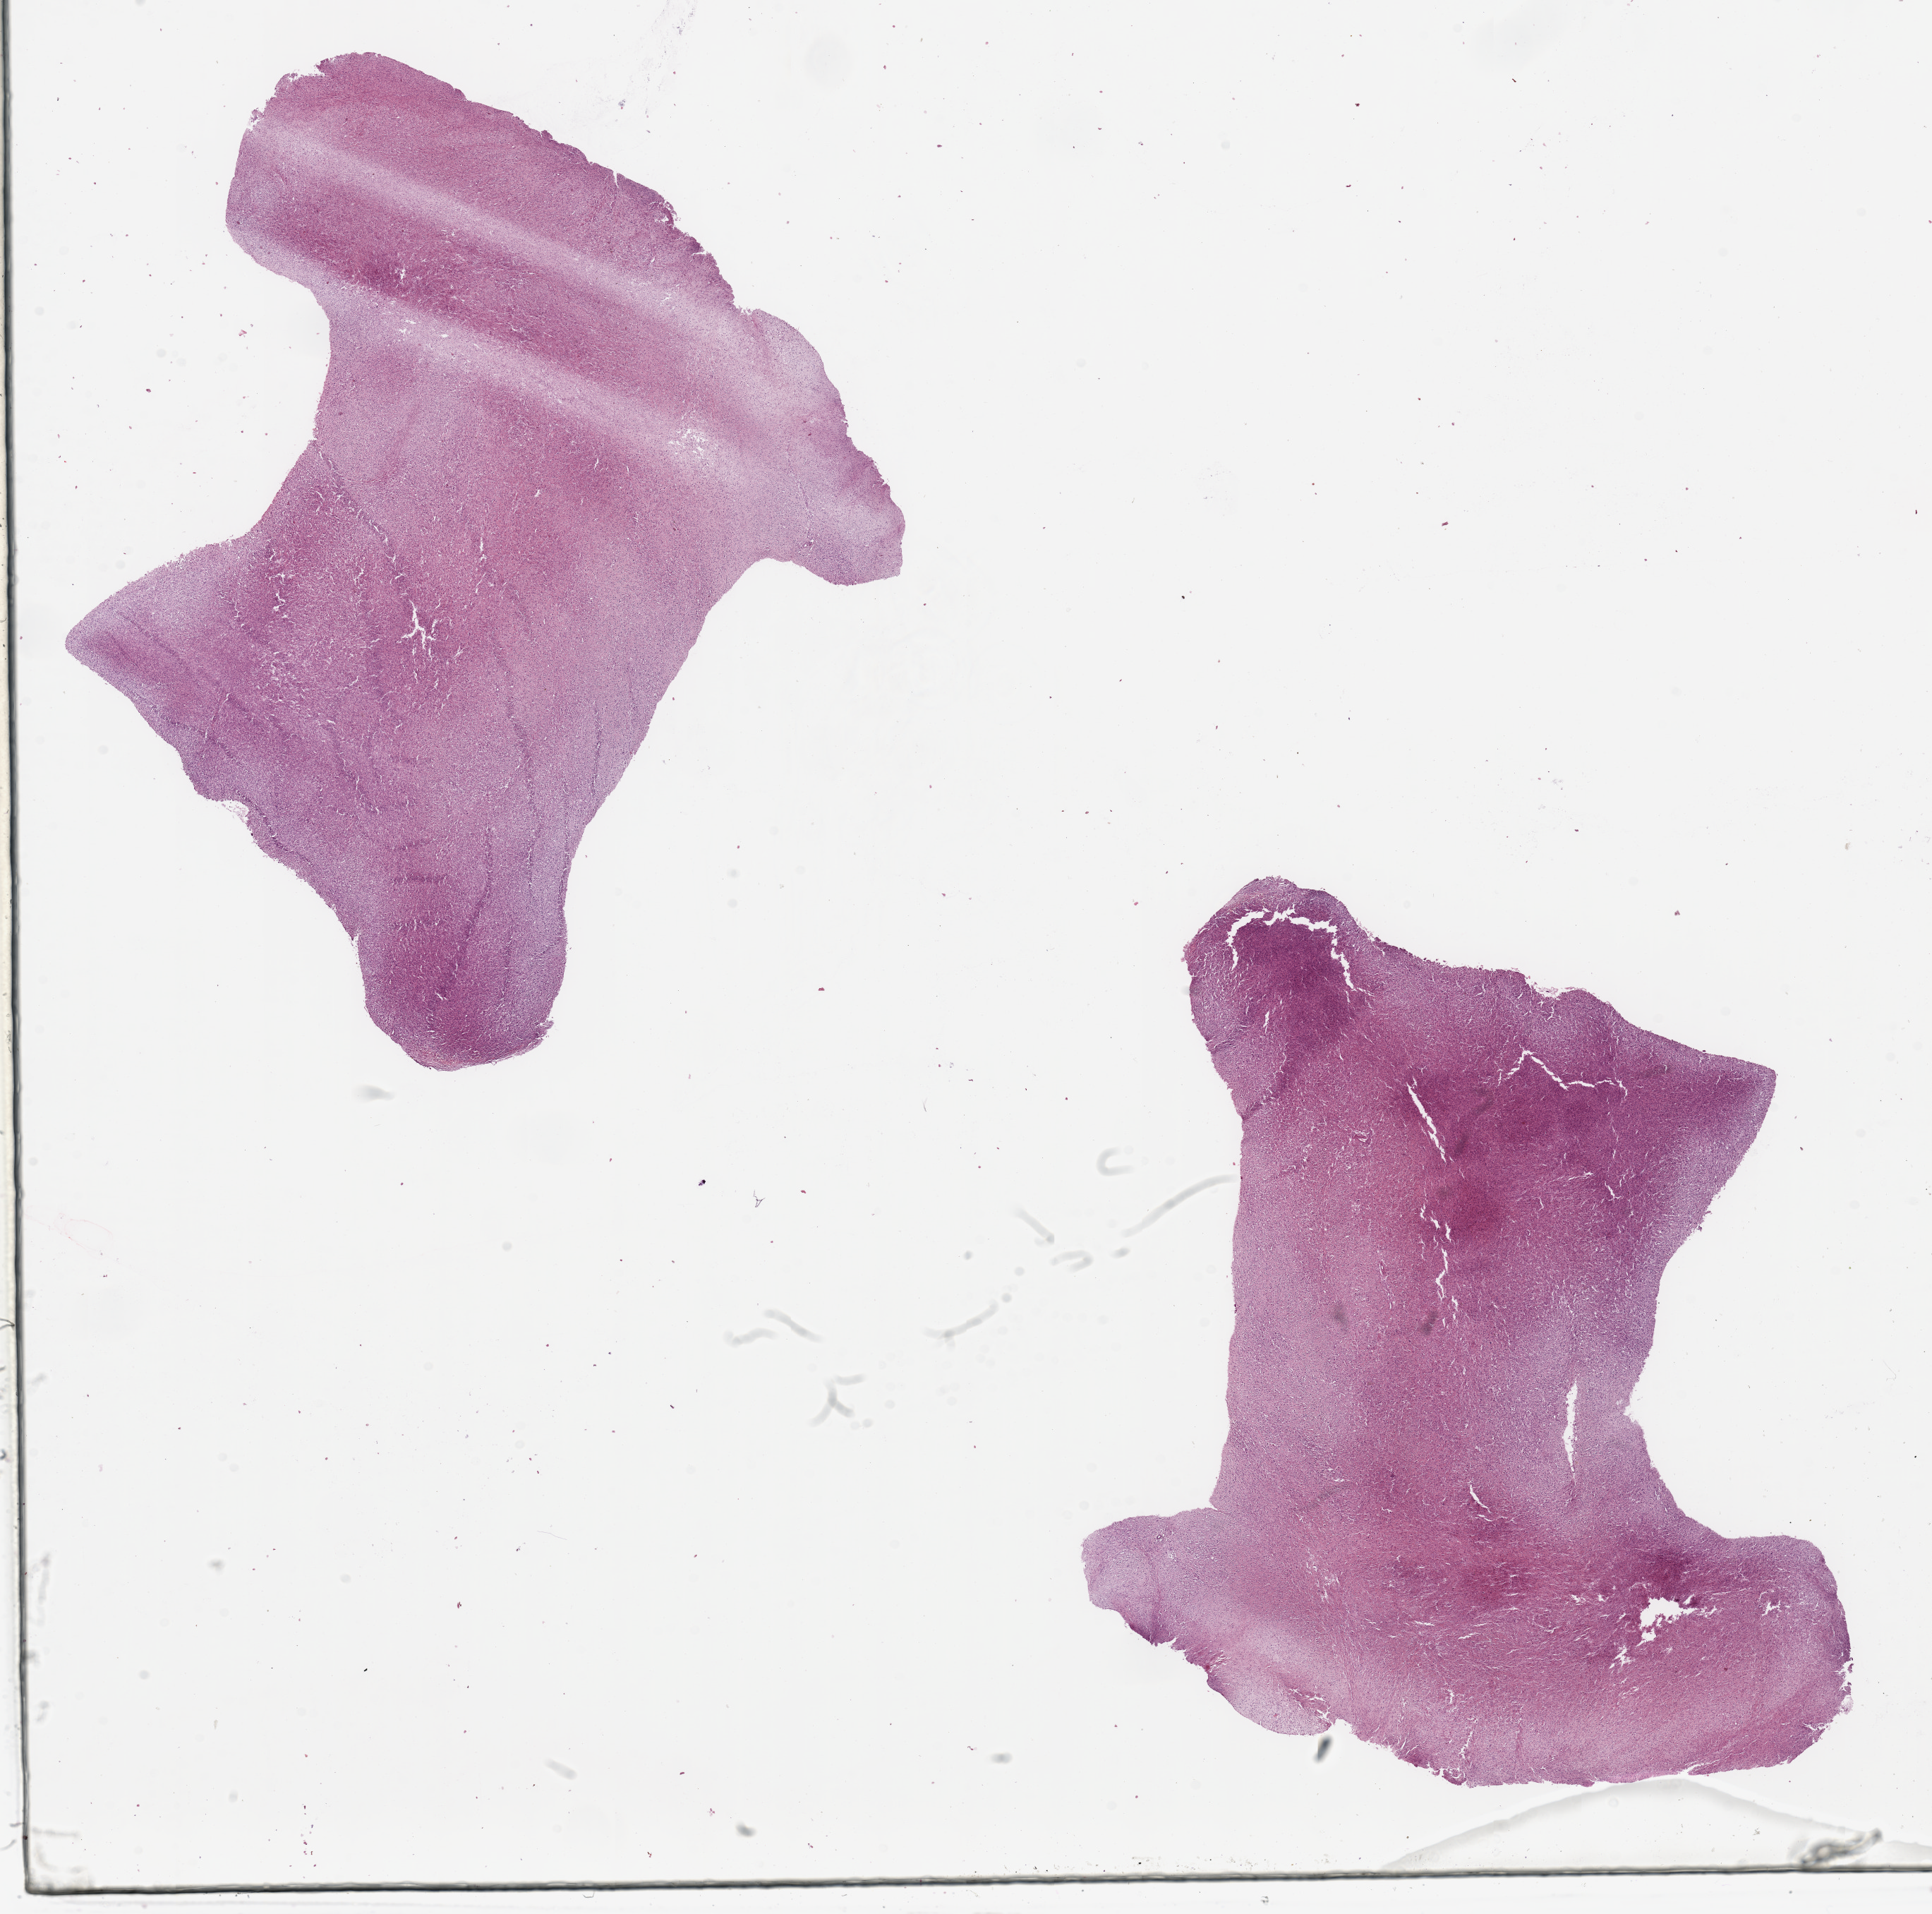
Whole-slide histology image, Hematoxylin and eosin (H&E) stained — a low-resolution overview of the entire scanned area, about 21.7 x 21.5 mm (slide scanned at 20x), tumour tissue sample. Female, 50 y/o.
Patient diagnosis (cohort enrolment): sarcoma (site not recorded at cohort level).